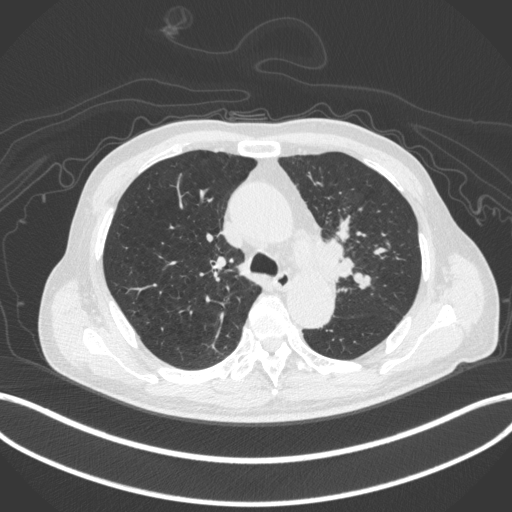
Chest CT, one axial slice. Position 299 of 420 along the scan axis. Reconstruction kernel B31f. 120 kVp. Lung window (W 1500 / L -600 HU). 1 mm slice thickness. 512 × 512 image matrix, field of view 400 × 400 mm. Male patient, age 77 years. From the clinical record (not read from this slice): clinical TNM (as recorded): T3 N1 M0.
Annotated regions visible in this slice (rectangle marked by the reading radiologist):
- lung tumour (recorded histology: adenocarcinoma): bounding box [x1, y1, x2, y2] px = [317, 233, 359, 285]